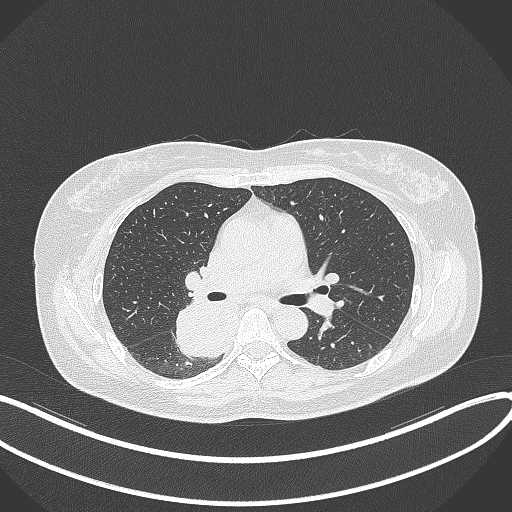
Chest CT, one axial slice; slice 214 of 331 in the series (ordered by position); lung window (W 1500 / L -600 HU); 1 mm slice thickness; 512 × 512 image matrix, field of view 400 × 400 mm. Female patient, age 54 years. Case-level facts recorded for this patient, not image findings: clinical TNM (as recorded): T4 N0 M0.
Structures marked on this image (rectangle marked by the reading radiologist):
- lung tumour (recorded histology: adenocarcinoma): box from (x=173, y=298) to (x=233, y=364) px